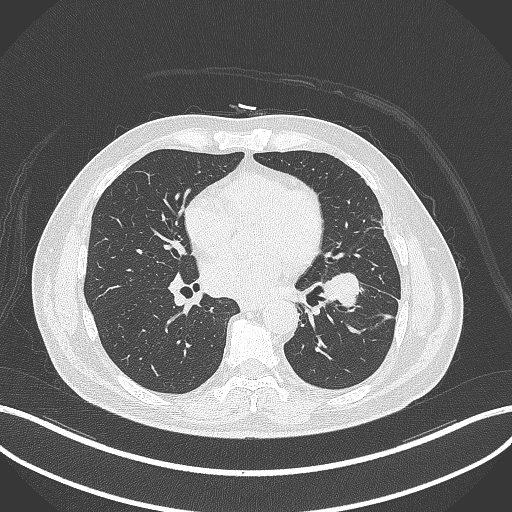
Chest CT, one axial slice; 120 kVp; lung window (W 1500 / L -600 HU); 1 mm slice thickness; 512 × 512 image matrix. Patient: male, 68 years. From the clinical record (not read from this slice): clinical TNM (as recorded): T2b N0 M0.
Outlined on this slice (bounding box drawn by a radiologist):
- lung tumour (recorded histology: squamous cell carcinoma): bounding box (x1, y1, x2, y2) in pixels: (322, 268, 365, 313)